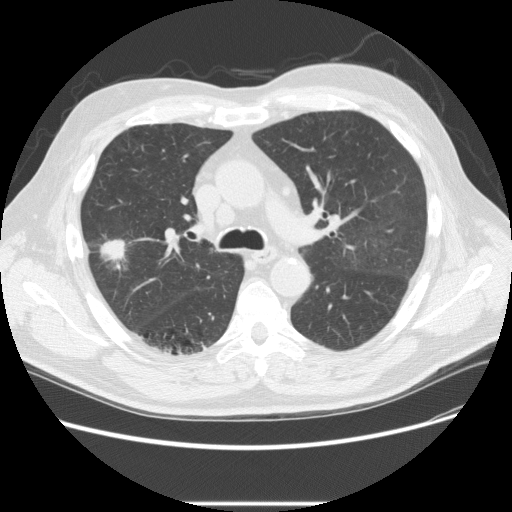
Low-dose screening chest CT, one axial slice; slice 148 of 233 in the series (ordered by position); lung window (W 1500 / L -600 HU); 2.5 mm slice thickness; 512 × 512 image matrix, field of view 380 × 380 mm.
Structures marked on this image (outlined manually by an expert reader):
- lesion 2 (tumor, upper lobe of right lung): box from (x=100, y=239) to (x=126, y=261) px